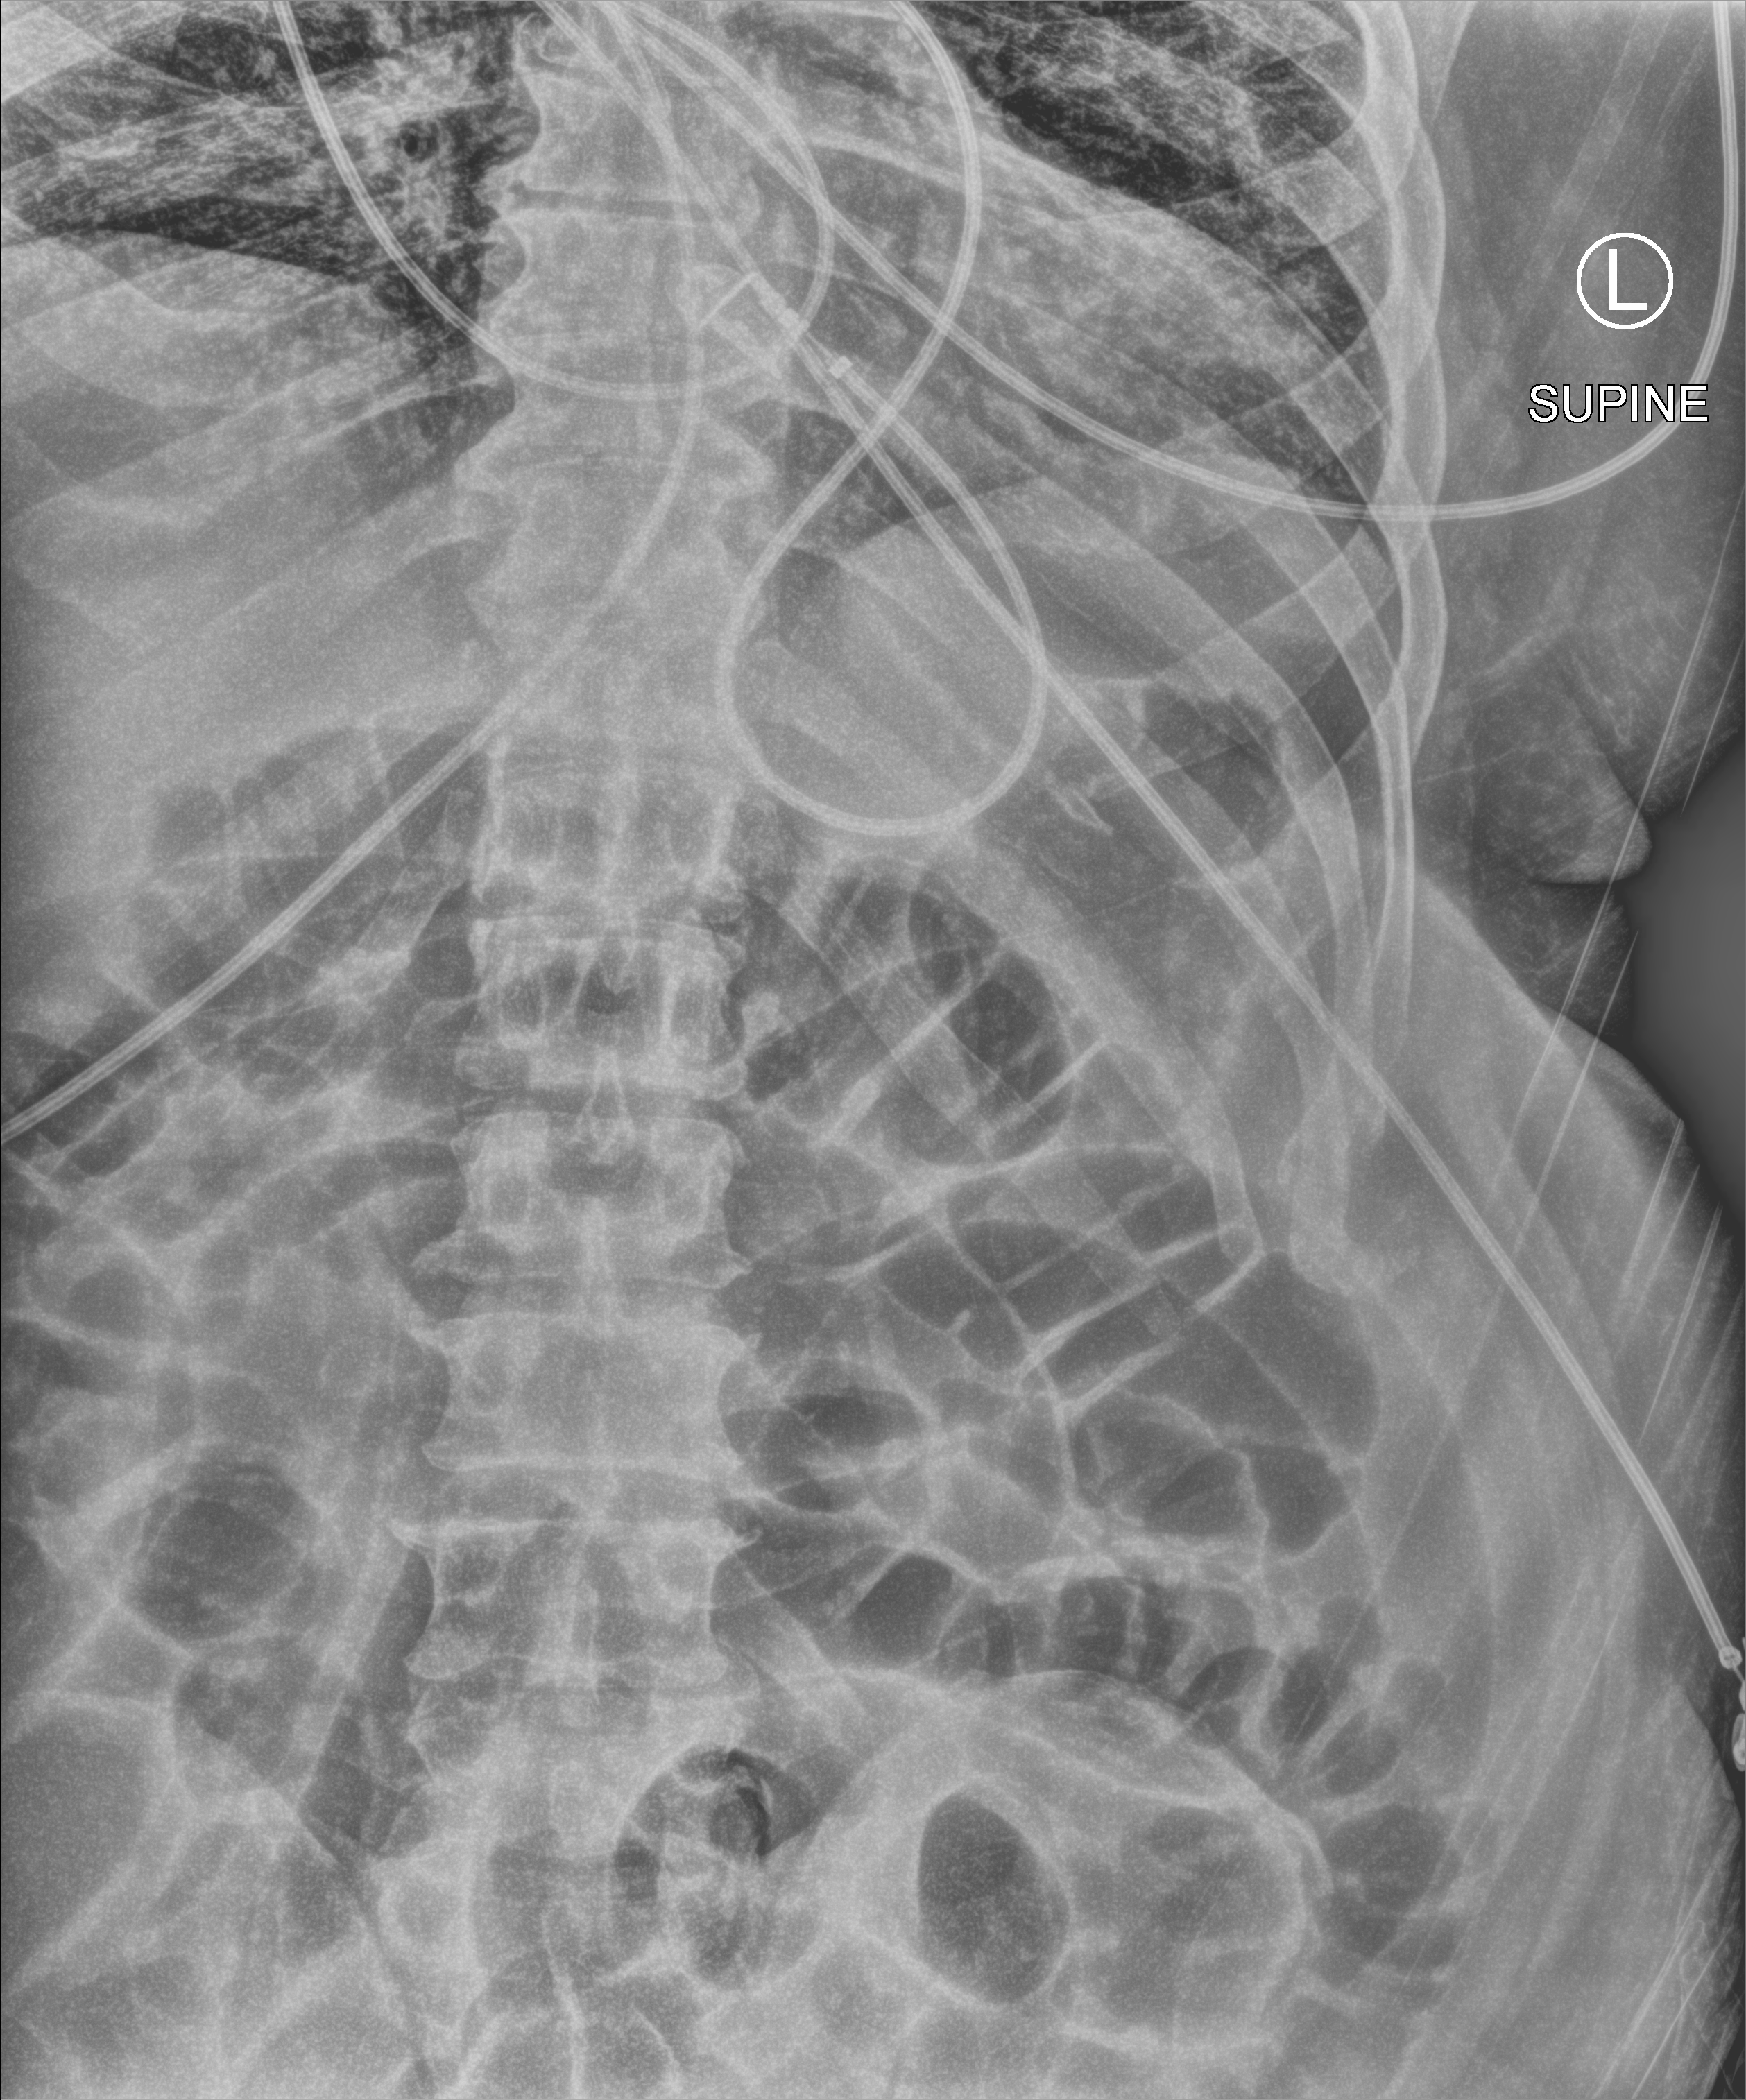
Bedside abdomen radiograph (computed radiography); anteroposterior (AP) projection. Patient hospitalised with COVID-19; male, aged 18–59 years.
From the hospital-stay record, not from the radiograph (when in the stay this image was taken is not recorded): length of hospital stay: 41 days.